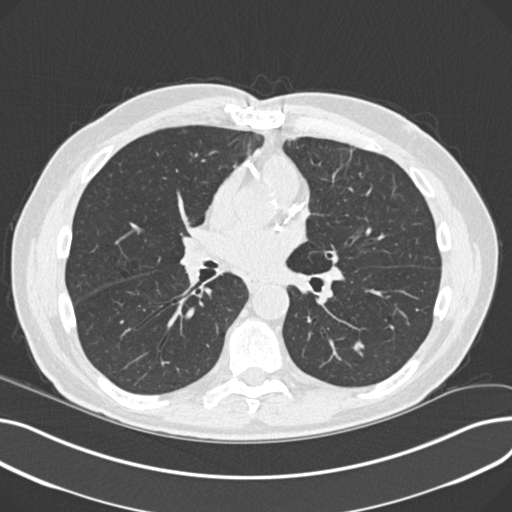
Low-dose screening chest CT, one axial slice. Slice 111 of 230 in the series (ordered by position). Reconstruction kernel B30f. 120 kVp. Lung window (W 1500 / L -600 HU). 2 mm slice thickness. 512 × 512 image matrix, field of view 372 × 372 mm.
Outlined on this slice (expert manual segmentation):
- lesion 3 (nodule, lower lobe of left lung): bounding box <353,340,365,351> (left, top, right, bottom; pixels)